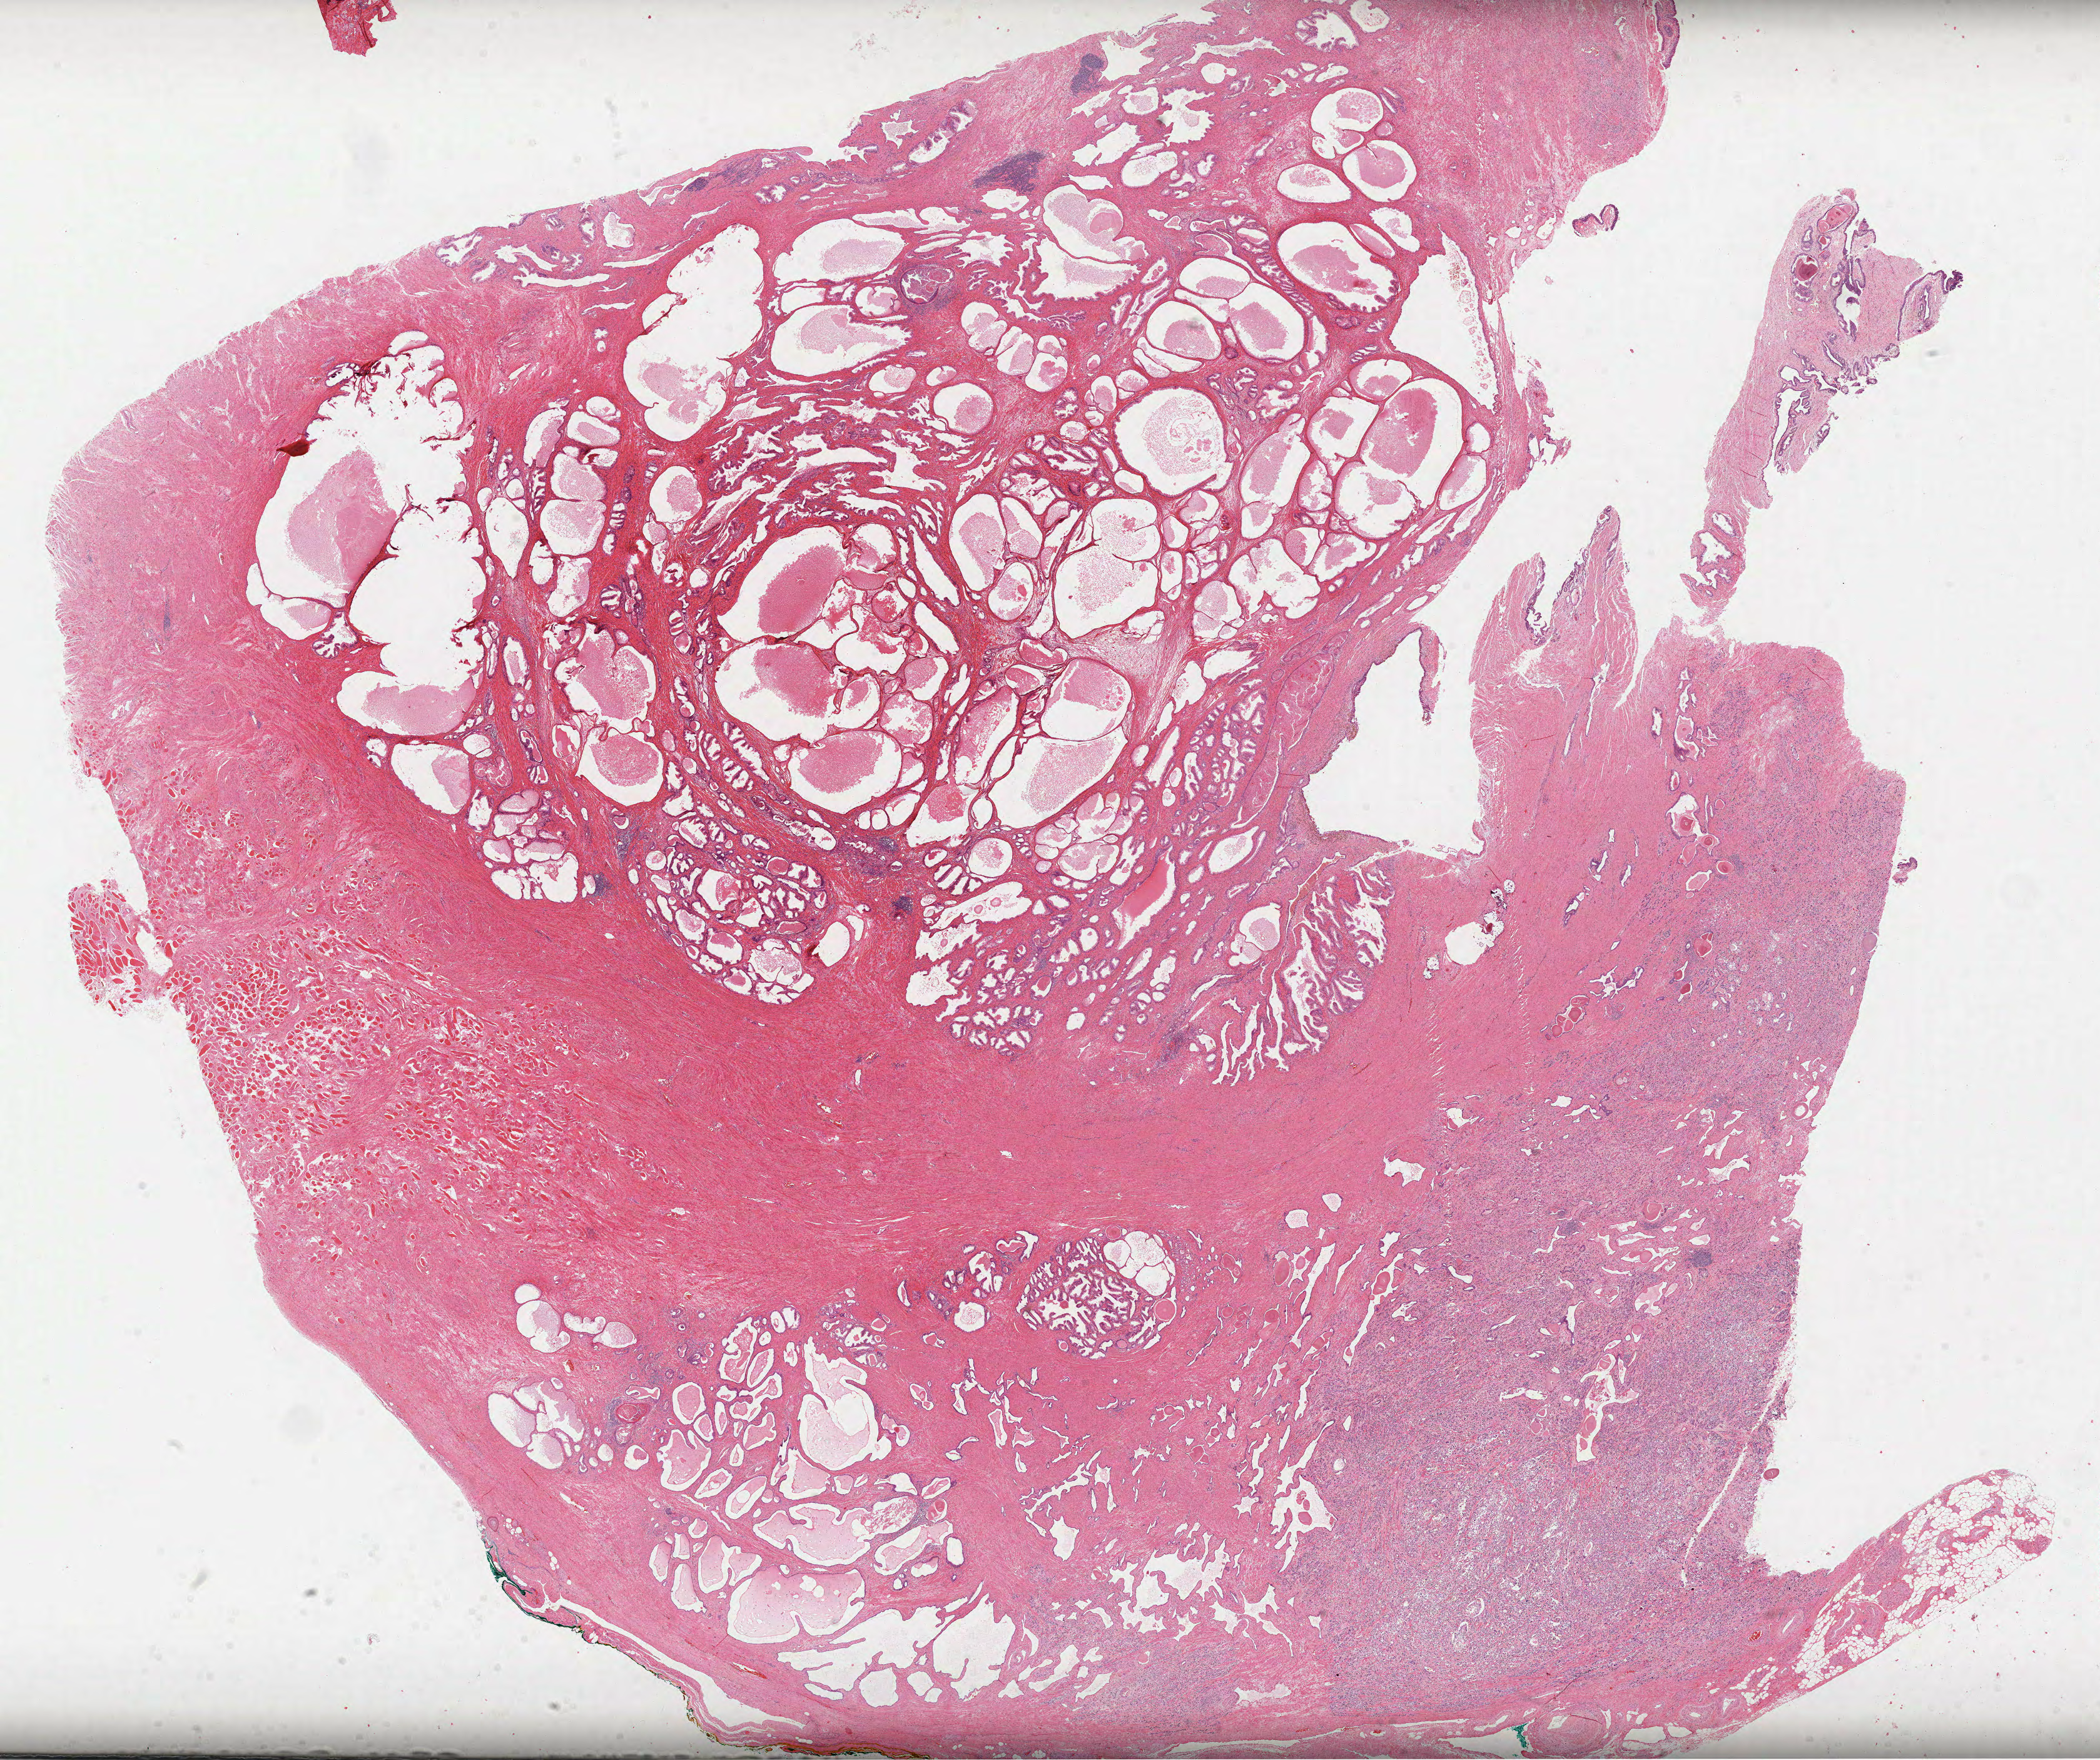
Whole-slide histology image, H&E — shown as a low-resolution overview of the whole scanned area (about 27.1 x 22.7 mm); formalin-fixed paraffin-embedded (FFPE) diagnostic section; sample: primary tumour, prostate. Male, age 66 years at initial diagnosis.
Diagnosis: Acinar cell carcinoma (prostate gland).